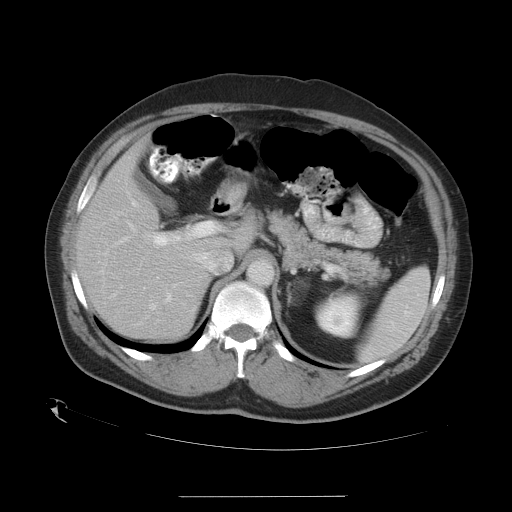
Contrast-enhanced abdominal CT, one axial slice. Slice 20 of 35 in the series (ordered by position). 120 kVp. Intravenous contrast given. Soft-tissue window (W 400 / L 40 HU). 7.5 mm slice thickness. 512 × 512 image matrix. Male patient, age 67 years. From the clinical record (not read from this slice): diagnosis: colorectal cancer liver metastases, imaged before liver resection; multiple liver metastases: no; largest metastasis: 2.3 cm.
Annotated regions visible in this slice (outlined manually by an expert reader):
- hepatic veins: bounding box (x1, y1, x2, y2) in pixels: (112, 201, 155, 309)
- liver: (76, 146, 242, 340)
- planned liver remnant (the part of the liver to remain after resection): (79, 146, 242, 340)
- portal vein (with intrahepatic branches): (116, 222, 215, 262)